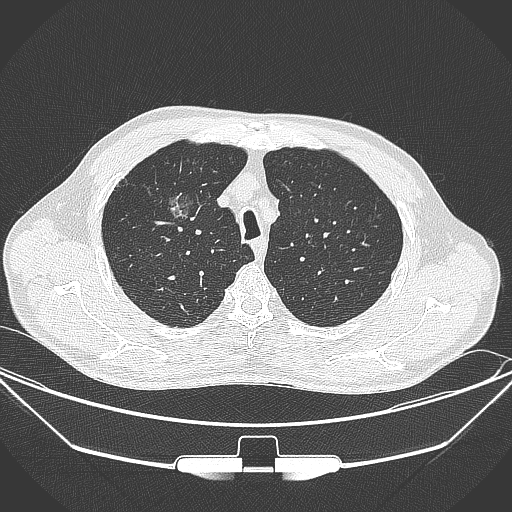
Chest CT, one axial slice. Slice 272 of 355 in the series (ordered by position). Lung window (W 1500 / L -600 HU). 1 mm slice thickness. 512 × 512 image matrix, field of view 399 × 399 mm. Patient: male, 67 years. Case-level facts recorded for this patient, not image findings: clinical TNM (as recorded): T1c N0 M0.
Outlined on this slice (bounding box drawn by a radiologist):
- lung tumour (recorded histology: adenocarcinoma): bounding box (x1, y1, x2, y2) in pixels: (159, 186, 203, 228)